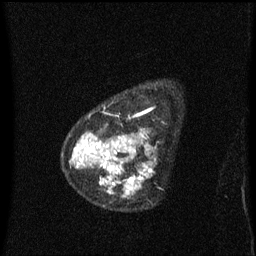
Breast MRI (dynamic contrast-enhanced), one sagittal slice; slice 48 of 60 in the series (ordered by position); dynamic contrast-enhanced series, image 2 of 3 at this slice position (ordered by acquisition); 1.5 T; TE 4.2 ms, TR 8.4 ms; 256 × 256 image matrix, field of view 200 × 200 mm. Female patient, age 48 years. From the clinical record (not read from this slice): setting: breast cancer imaged before/during neoadjuvant chemotherapy; receptor status: HR-positive, HER2-negative.
Outlined on this slice (semi-automatically segmented with operator editing):
- analysis volume of interest (the breast-tissue region the enhancement analysis was run in; not a lesion): bounding box [x1, y1, x2, y2] px = [80, 88, 153, 199]
- tumour enhancement mask (voxels above the 70 % enhancement threshold inside the analysis volume of interest): [82, 135, 153, 195]